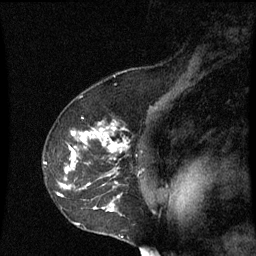
Breast MRI (dynamic contrast-enhanced), one sagittal slice; position 45 of 60 along the scan axis; dynamic contrast-enhanced series, image 2 of 3 at this slice position (ordered by acquisition); 1.5 T; TE 4.2 ms, TR 8.9 ms; 2 mm slice thickness; 256 × 256 image matrix. Female patient, age 53 years. Case-level facts recorded for this patient, not image findings: setting: breast cancer imaged before/during neoadjuvant chemotherapy; receptor status: HR-positive, HER2-negative.
Structures marked on this image (semi-automatic segmentation, software-assisted and operator-edited):
- analysis volume of interest (the breast-tissue region the enhancement analysis was run in; not a lesion): box from (x=44, y=128) to (x=157, y=227) px
- tumour enhancement mask (voxels above the 70 % enhancement threshold inside the analysis volume of interest): (x=58, y=128)–(x=125, y=211)